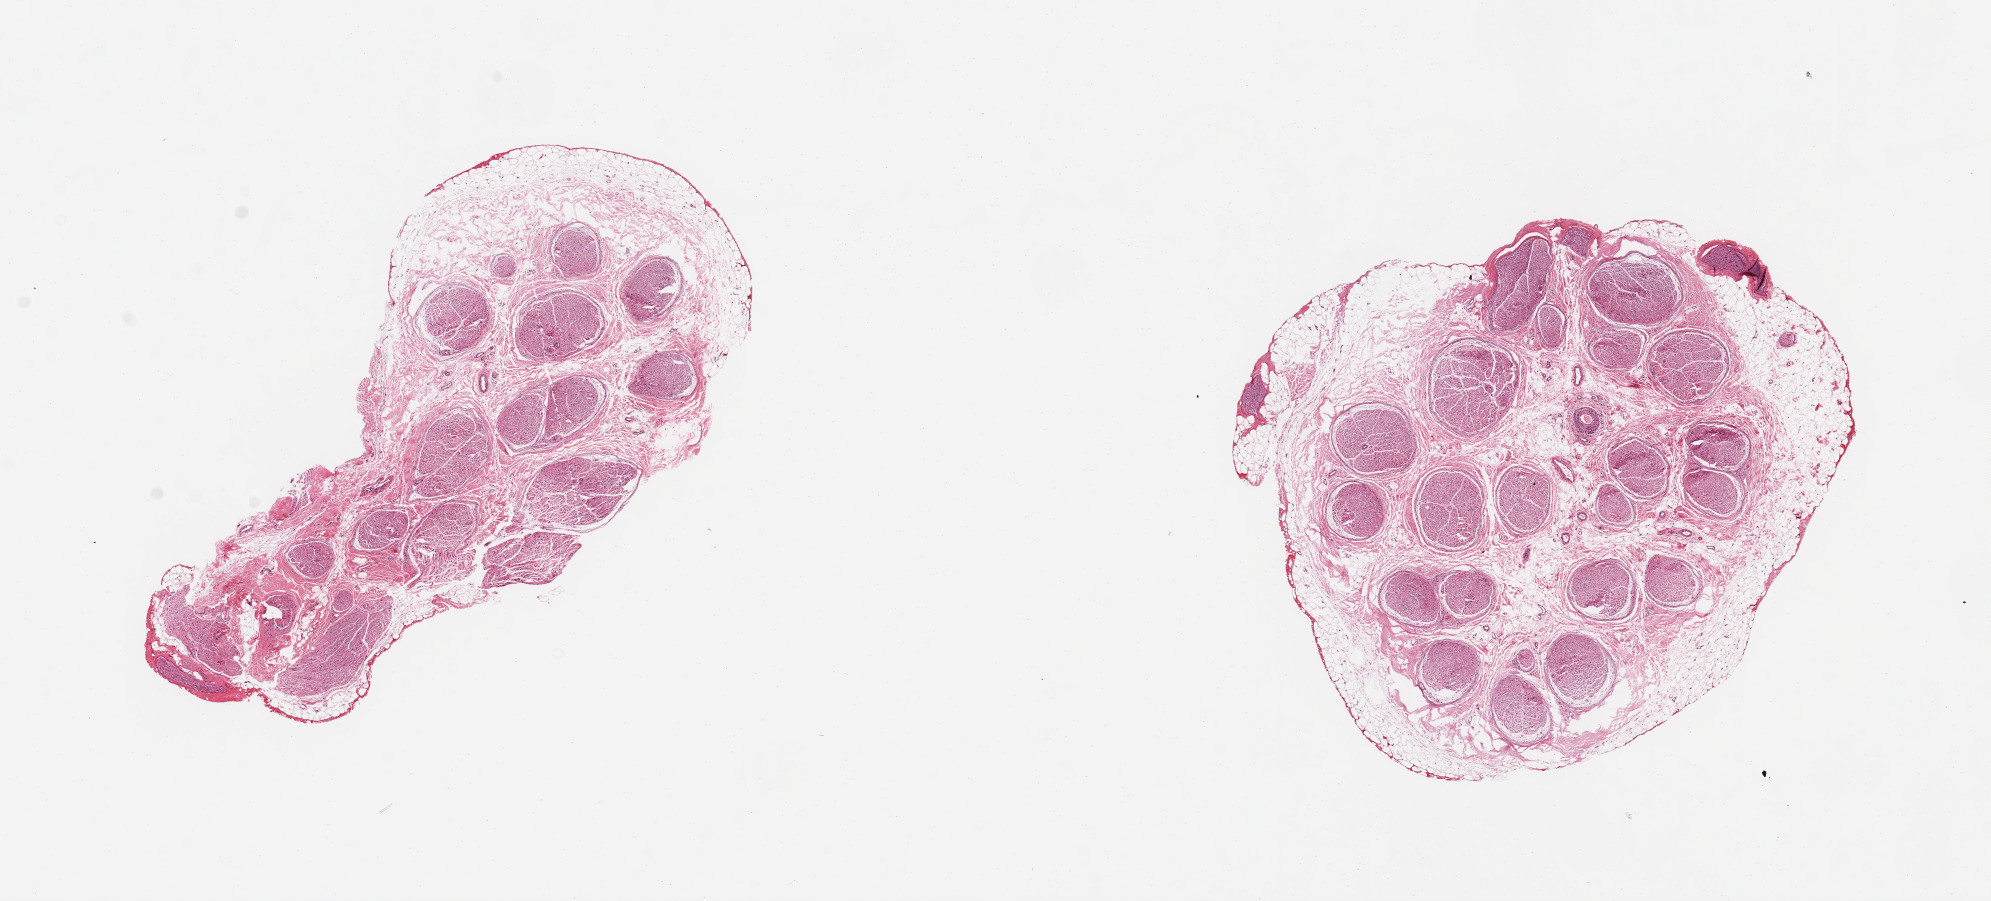
Digitized H&E-stained section, brightfield, shown as a low-resolution overview of the whole scanned area (about 15.8 x 7.1 mm); PAXgene-fixed, paraffin-embedded tissue; section of tibial nerve (target tissue); donor tissue sample. Female donor.
Review note (as recorded): 2 pieces; up to 40% internal/external fat.